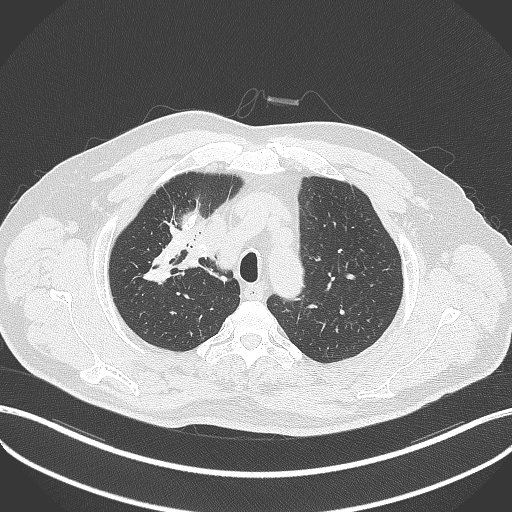
Chest CT, one axial slice. 120 kVp. Lung window (W 1500 / L -600 HU). 1 mm slice thickness. 512 × 512 image matrix, field of view 400 × 400 mm. Patient: male, 60 years. Case-level facts recorded for this patient, not image findings: clinical TNM (as recorded): T1b N1 M0.
Structures marked on this image (bounding box drawn by a radiologist):
- lung tumour (recorded histology: squamous cell carcinoma): bounding box [x1, y1, x2, y2] px = [179, 247, 205, 273]